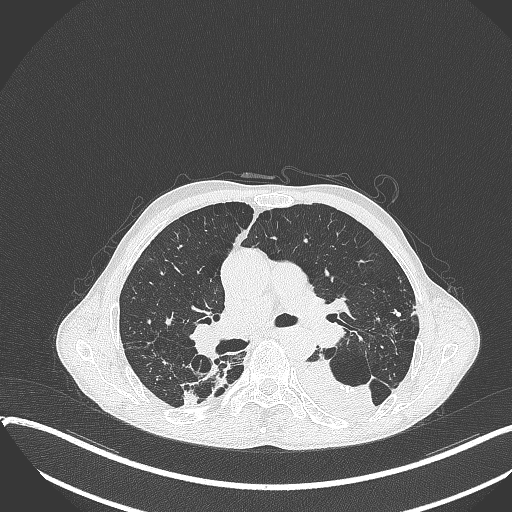
Chest CT, one axial slice. Position 231 of 401 along the scan axis. Reconstruction kernel B70f. 120 kVp. Lung window (W 1500 / L -600 HU). 1 mm slice thickness. 512 × 512 image matrix, field of view 400 × 400 mm. Male patient, age 57 years. Case-level facts recorded for this patient, not image findings: clinical TNM (as recorded): T4 N0 M0.
Structures marked on this image (rectangle marked by the reading radiologist):
- lung tumour (recorded histology: squamous cell carcinoma): bounding box <292,354,380,426> (left, top, right, bottom; pixels)